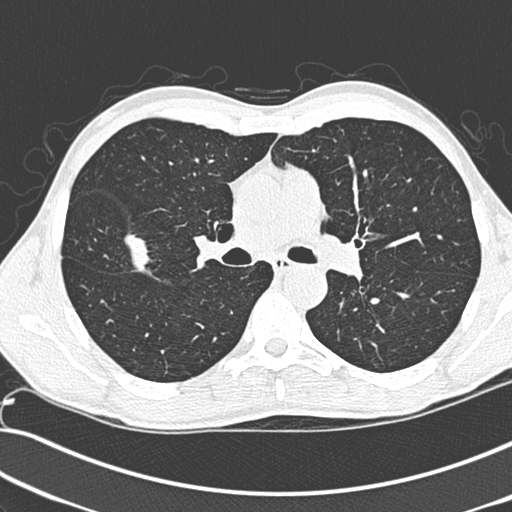
Low-dose screening chest CT, one axial slice; position 184 of 281 along the scan axis; 120 kVp; lung window (W 1500 / L -600 HU); 1.3 mm slice thickness; 512 × 512 image matrix, field of view 341 × 341 mm.
Structures marked on this image (outlined manually by an expert reader):
- lesion 1 (tumor, upper lobe of right lung): box from (x=124, y=234) to (x=151, y=275) px